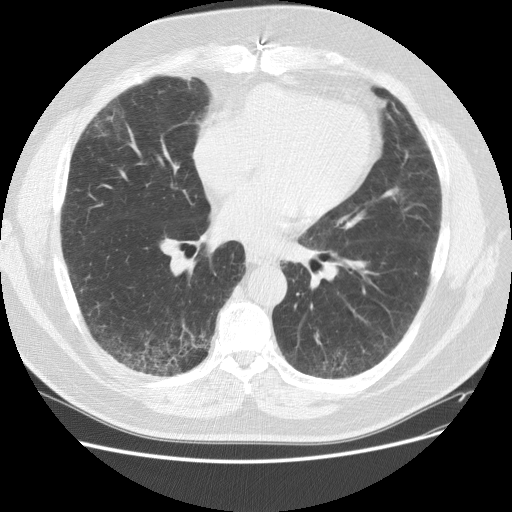
Chest CT (low-dose screening protocol), one axial image, baseline annual screen, lung window (W 1500 / L -600 HU), 2.5 mm slice thickness, standard (soft-tissue) reconstruction kernel (STANDARD). Male, age 59 years at enrolment. Current smoker at enrolment.
Expert reader's lesion annotation, bounding box <83,93,131,143> (left, top, right, bottom; pixels). The screening reader recorded 2 non-calcified nodules or masses ≥4 mm on this exam (right middle lobe, right lower lobe); which of them this box marks is not recorded. Lung cancer was diagnosed 338 days after this screen: adenocarcinoma, NOS, right upper lobe, right middle lobe, moderately differentiated (G2), stage IA (AJCC 6th edition), 13 mm at pathology.